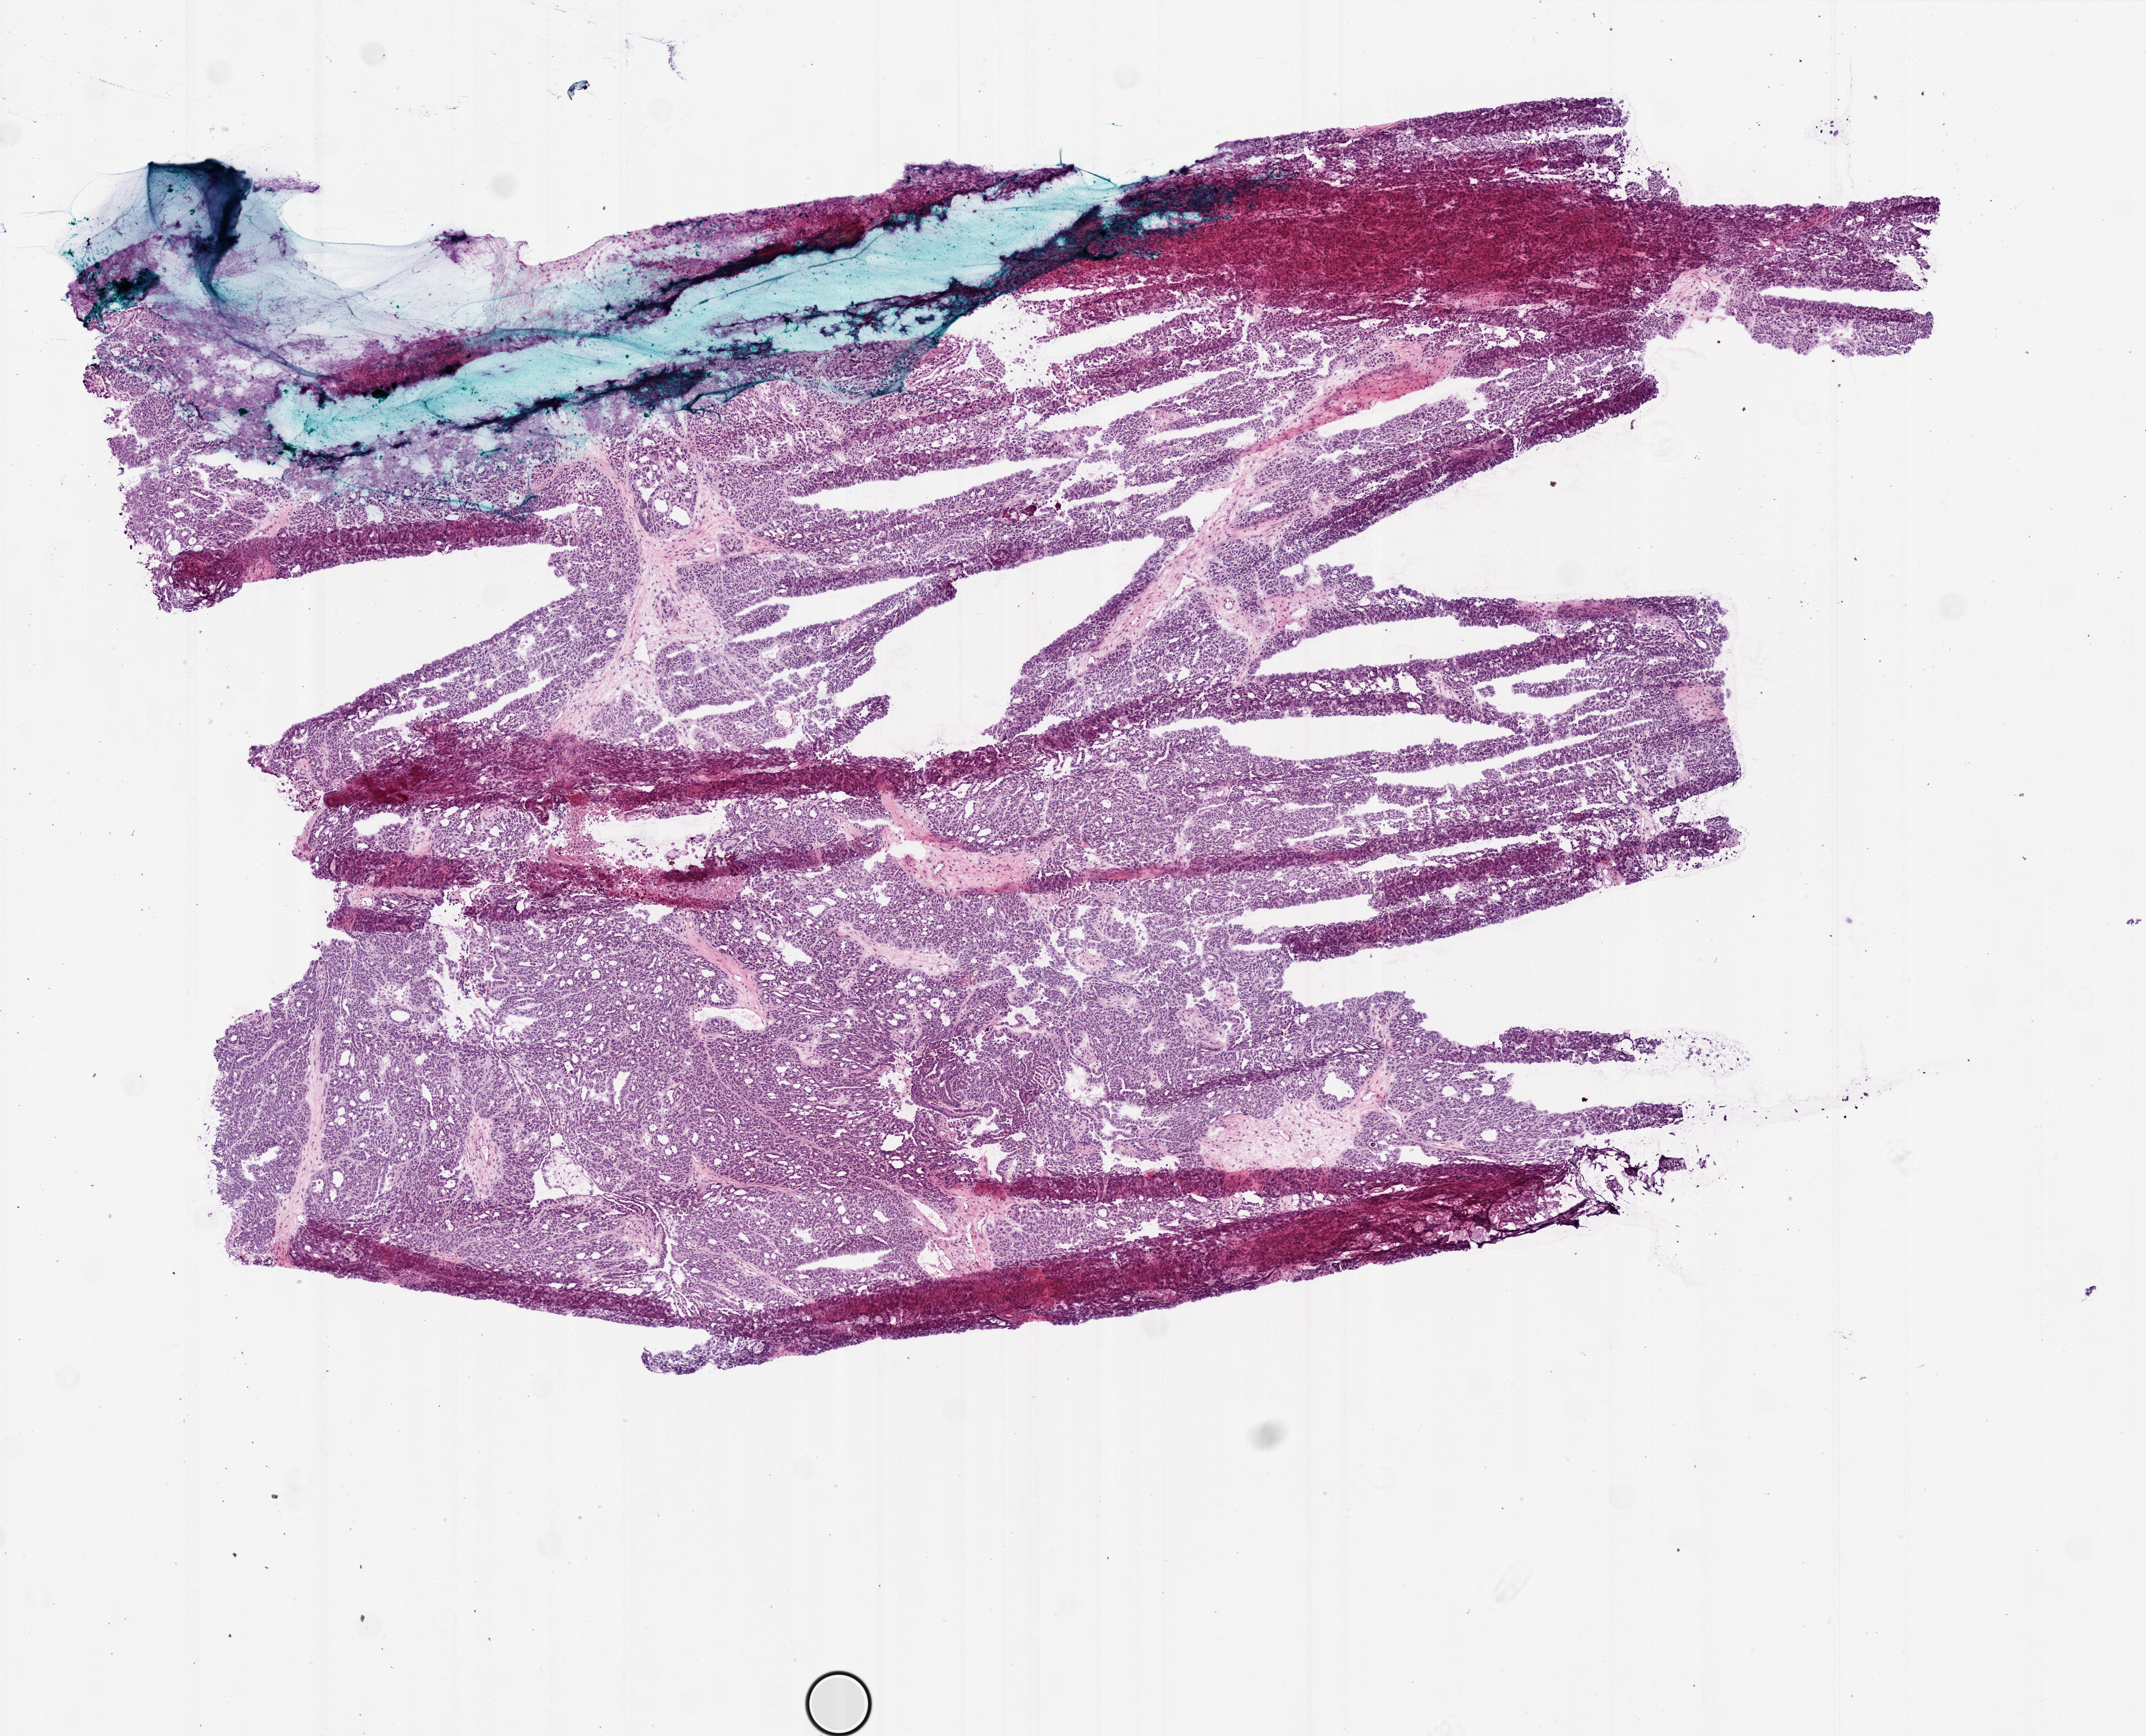
Whole-slide histology image, H&E — a low-resolution overview of the entire scanned area, about 8.0 x 6.5 mm. Frozen section. Ovary, primary tumour sample. Patient: female, age at initial diagnosis 70 years. Histologic grade: G3 (poorly differentiated). Slide review estimates, as recorded: tumour cells 95%, tumour nuclei 98%, normal cells 0%, stromal cells 5%, necrosis 0%.
FIGO stage: IIIC. Histologic diagnosis: Serous cystadenocarcinoma, NOS. Laterality: left.